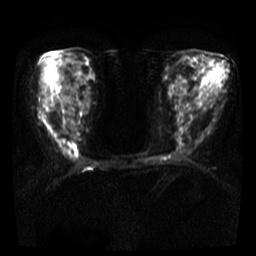
Breast MRI, one axial slice. Slice 15 of 36 in the series (ordered by position). Diffusion-weighted series; image 2 of 4 stored at this slice position (different b-values; order by instance number). 3 T. 256 × 256 image matrix, field of view 300 × 300 mm. Female patient.
Annotated regions visible in this slice (manually delineated by an expert):
- tumour on diffusion-weighted imaging: bounding box (x1, y1, x2, y2) in pixels: (59, 139, 69, 155)